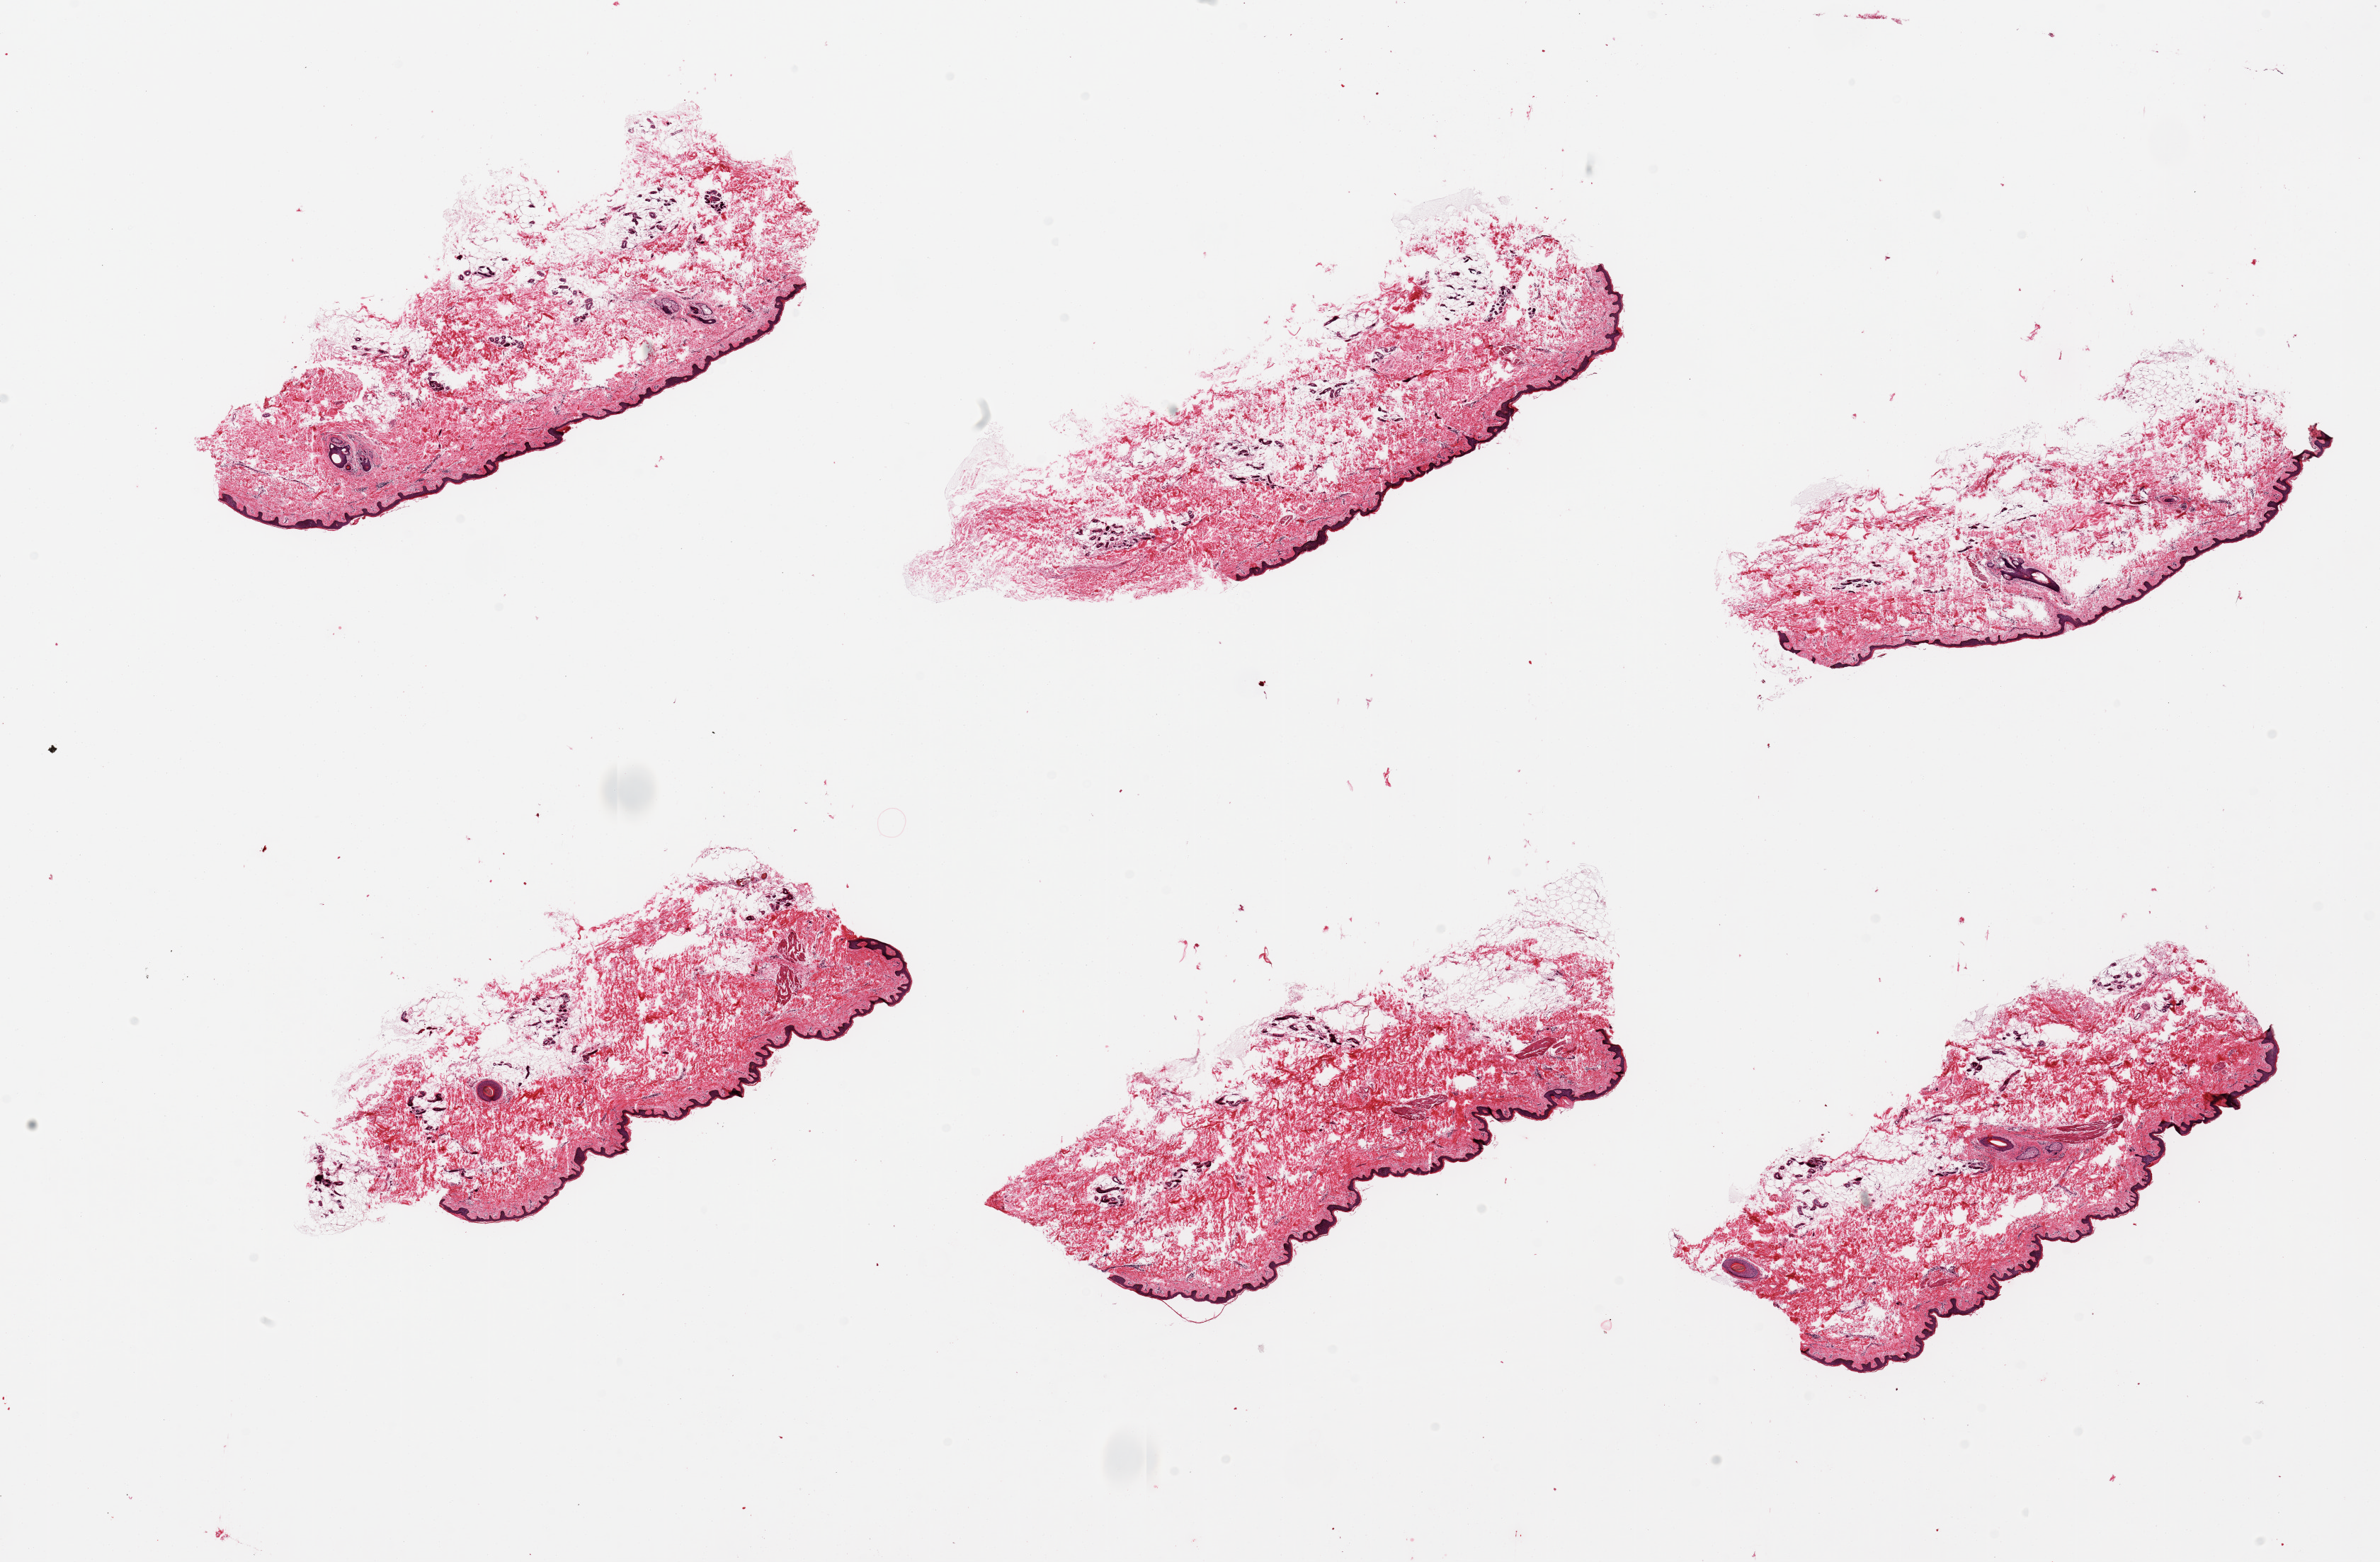
Whole-slide image, hematoxylin and eosin (H&E) stain, whole scanned area (about 26.6 x 17.4 mm, slide scanned at 20x) shown as a low-resolution overview; PAXgene-fixed paraffin-embedded (PFPE) section; target tissue: skin of suprapubic region; tissue donor sample. Donor: female.
- pathologist's review note for this sample: 6 pieces; edematous dermis with 20% fat